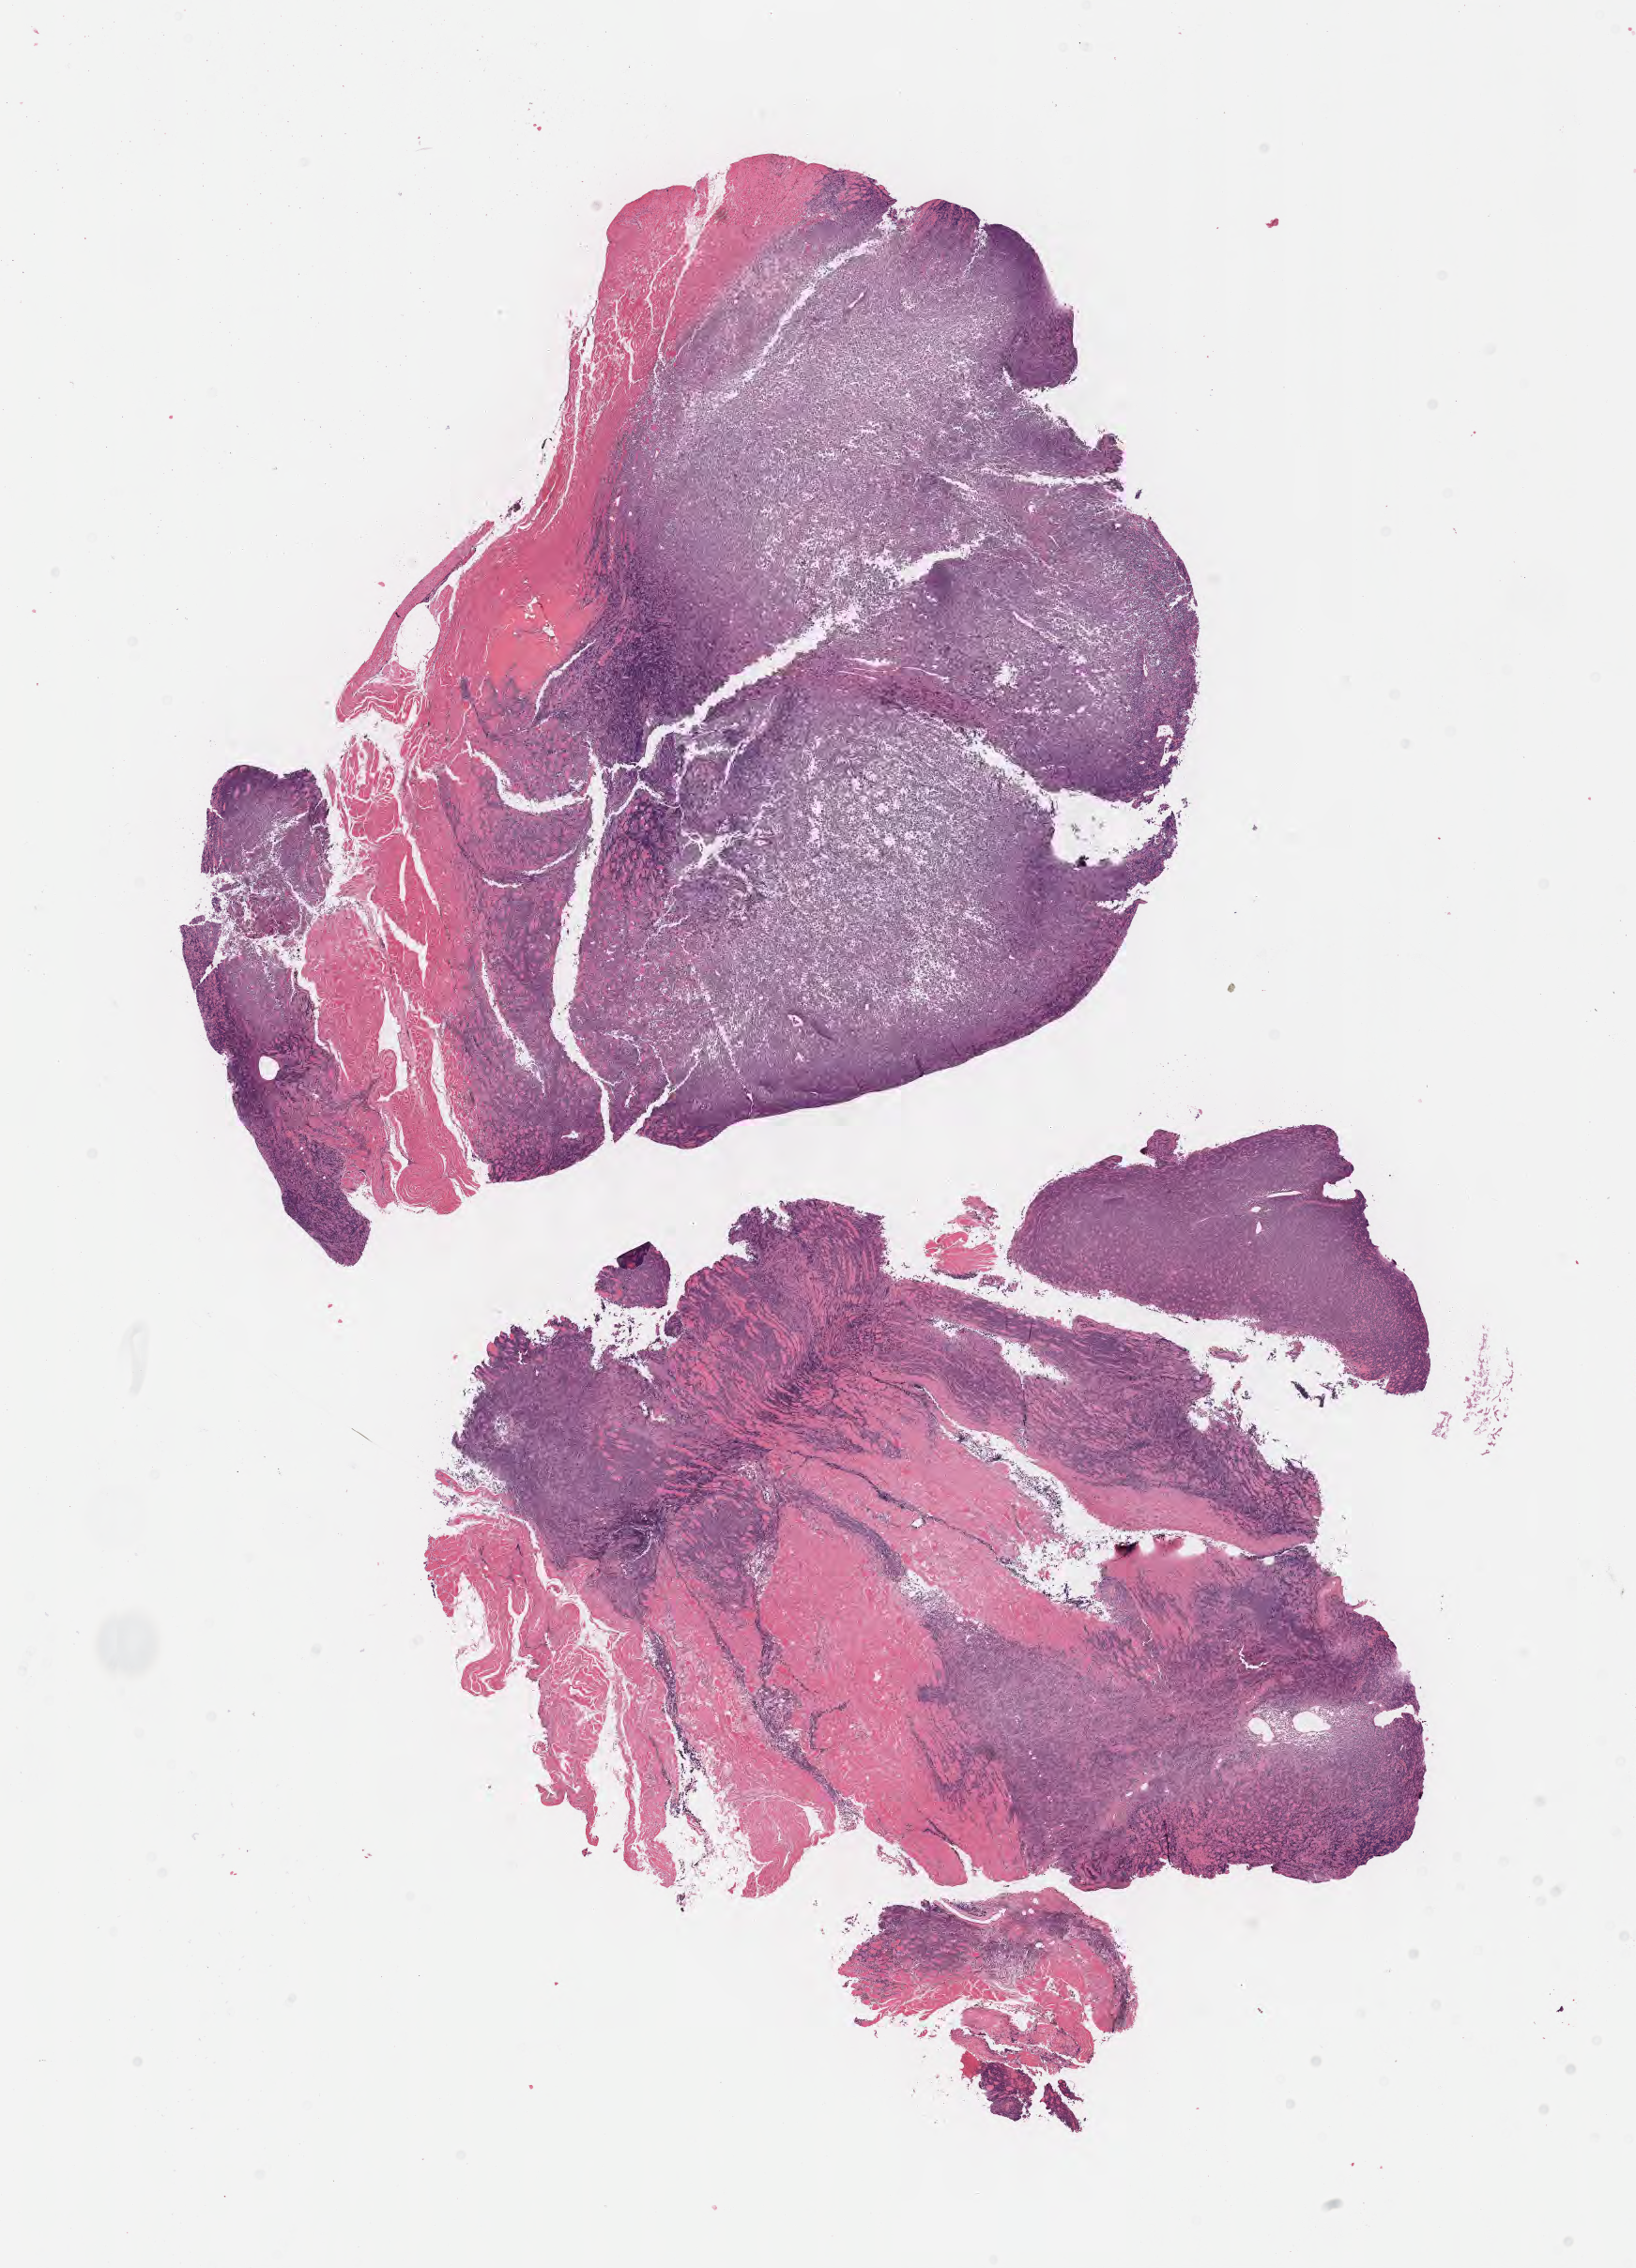
Whole-slide image, hematoxylin and eosin (H&E) stain, whole scanned area (about 14.1 x 19.5 mm) shown as a low-resolution overview, specimen: tumor tissue. Patient male; age 40 years.
Histologic diagnosis: Burkitt lymphoma, NOS.